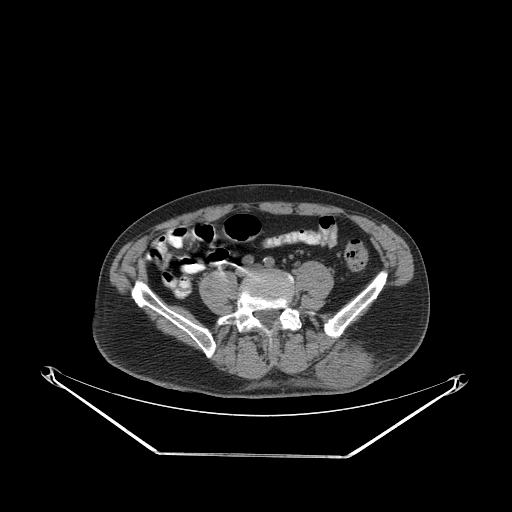
CT of an extremity soft-tissue mass (from a PET/CT study), one axial slice; slice 90 of 267 in the series (ordered by position); 140 kVp; soft-tissue window (W 400 / L 40 HU); 3.75 mm slice thickness; 512 × 512 image matrix, field of view 500 × 500 mm. Male patient. From the clinical record (not read from this slice): histological type: leiomyosarcoma; grade: intermediate; site of the primary tumour: left pelvis.
Structures marked on this image (expert contour drawn on MRI and transferred to this co-registered scan by the dataset authors):
- gross tumour volume (mass): bounding box [x1, y1, x2, y2] px = [317, 340, 375, 389]